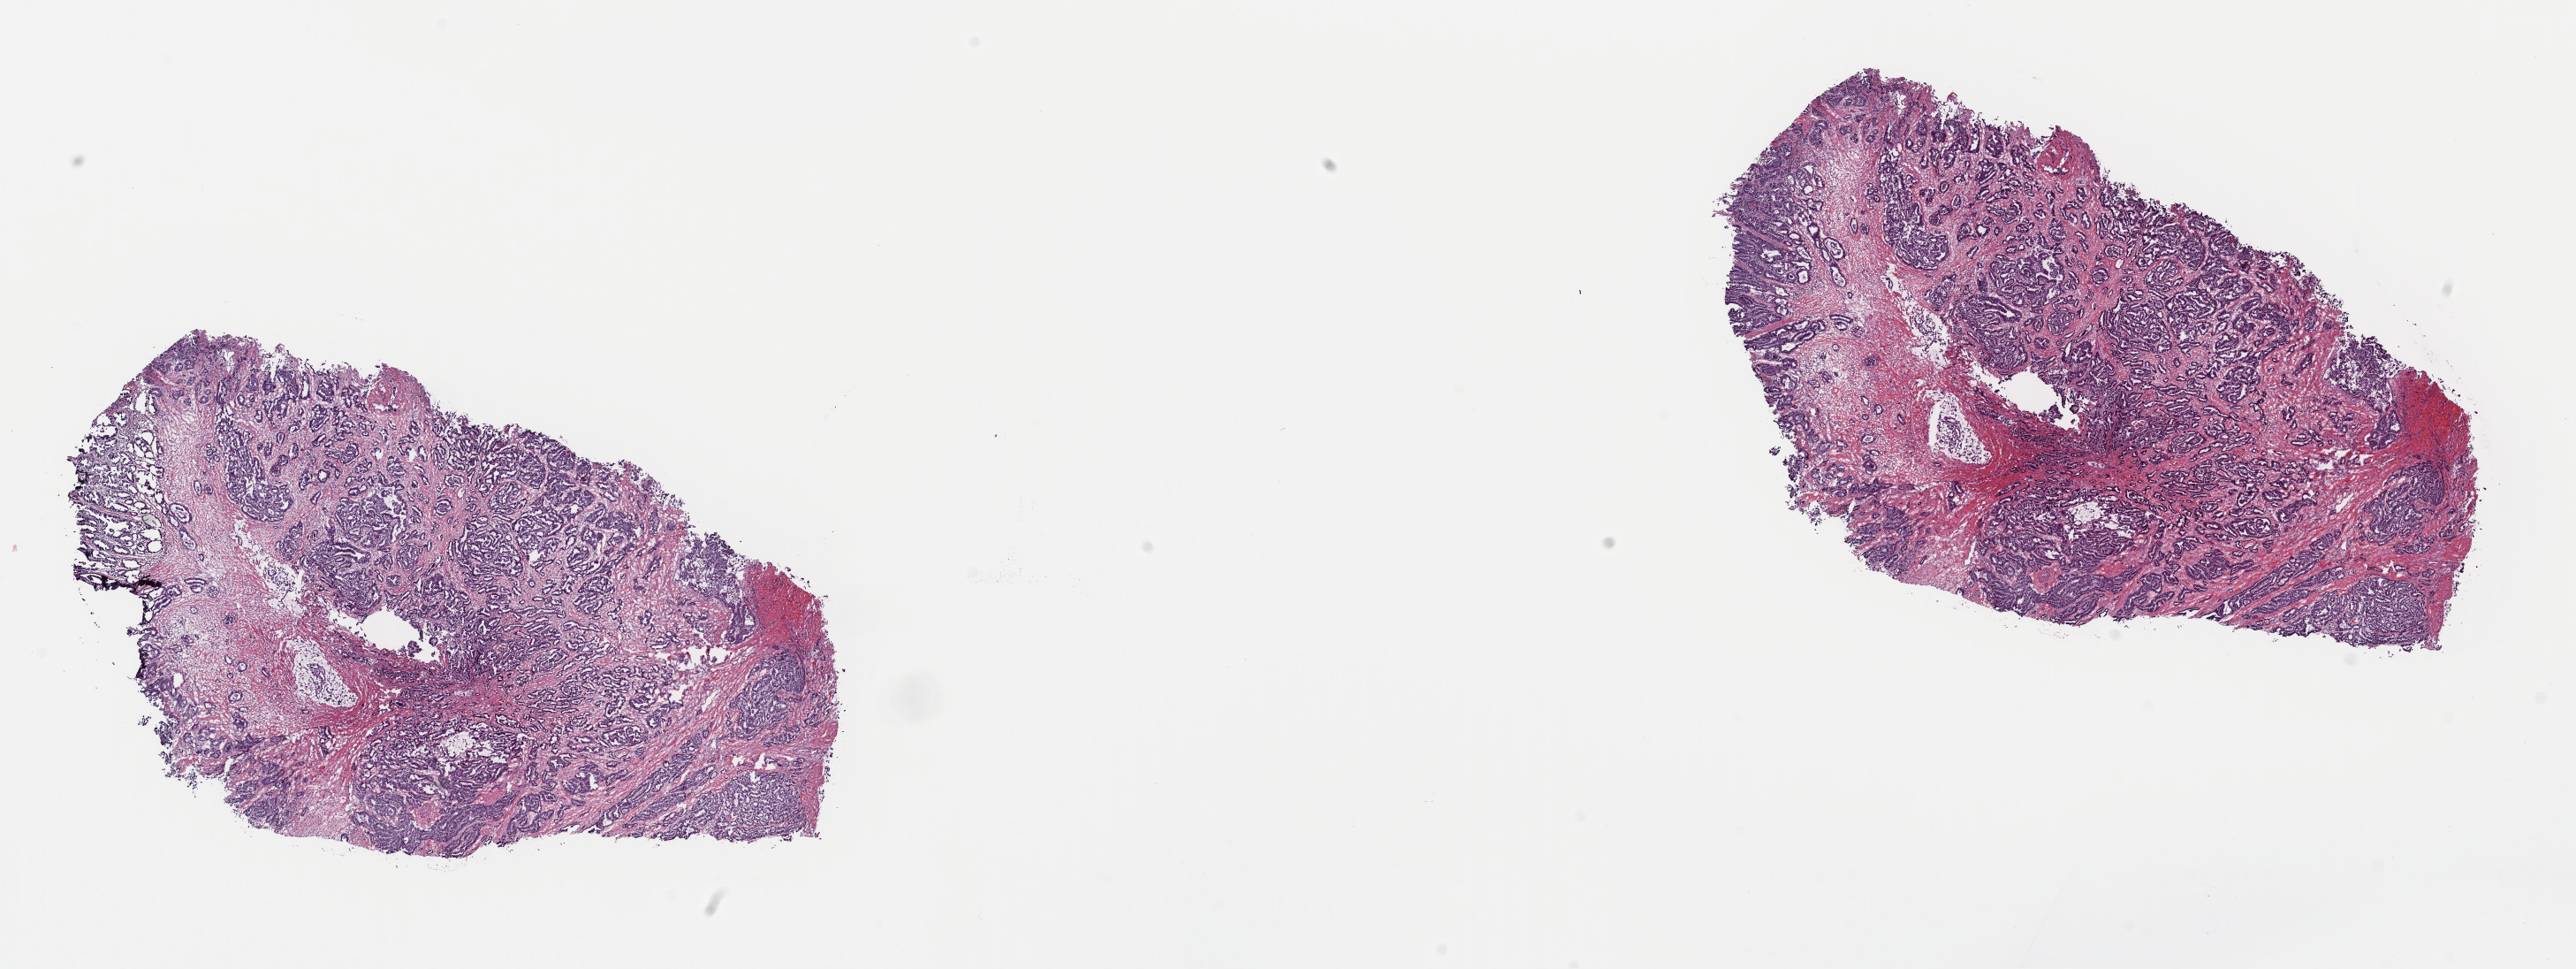
Digitized H&E tissue section (whole slide) — low-resolution overview of the scanned area, about 23.0 x 8.7 mm (from a 40x scan); frozen section from the top of the tissue portion; thyroid, primary tumour sample. Patient: female, age at initial diagnosis 58 years. Composition of this section per pathologist review: tumour cells 85%, tumour nuclei 95%, normal cells 0%, stromal cells 15%, necrosis 0%. Infiltration values recorded for this section: lymphocyte infiltration 0%, monocyte infiltration 0%, neutrophil infiltration 0%.
AJCC pathologic stage: III (7th edition). Pathologic diagnosis: Papillary carcinoma, columnar cell (thyroid gland).